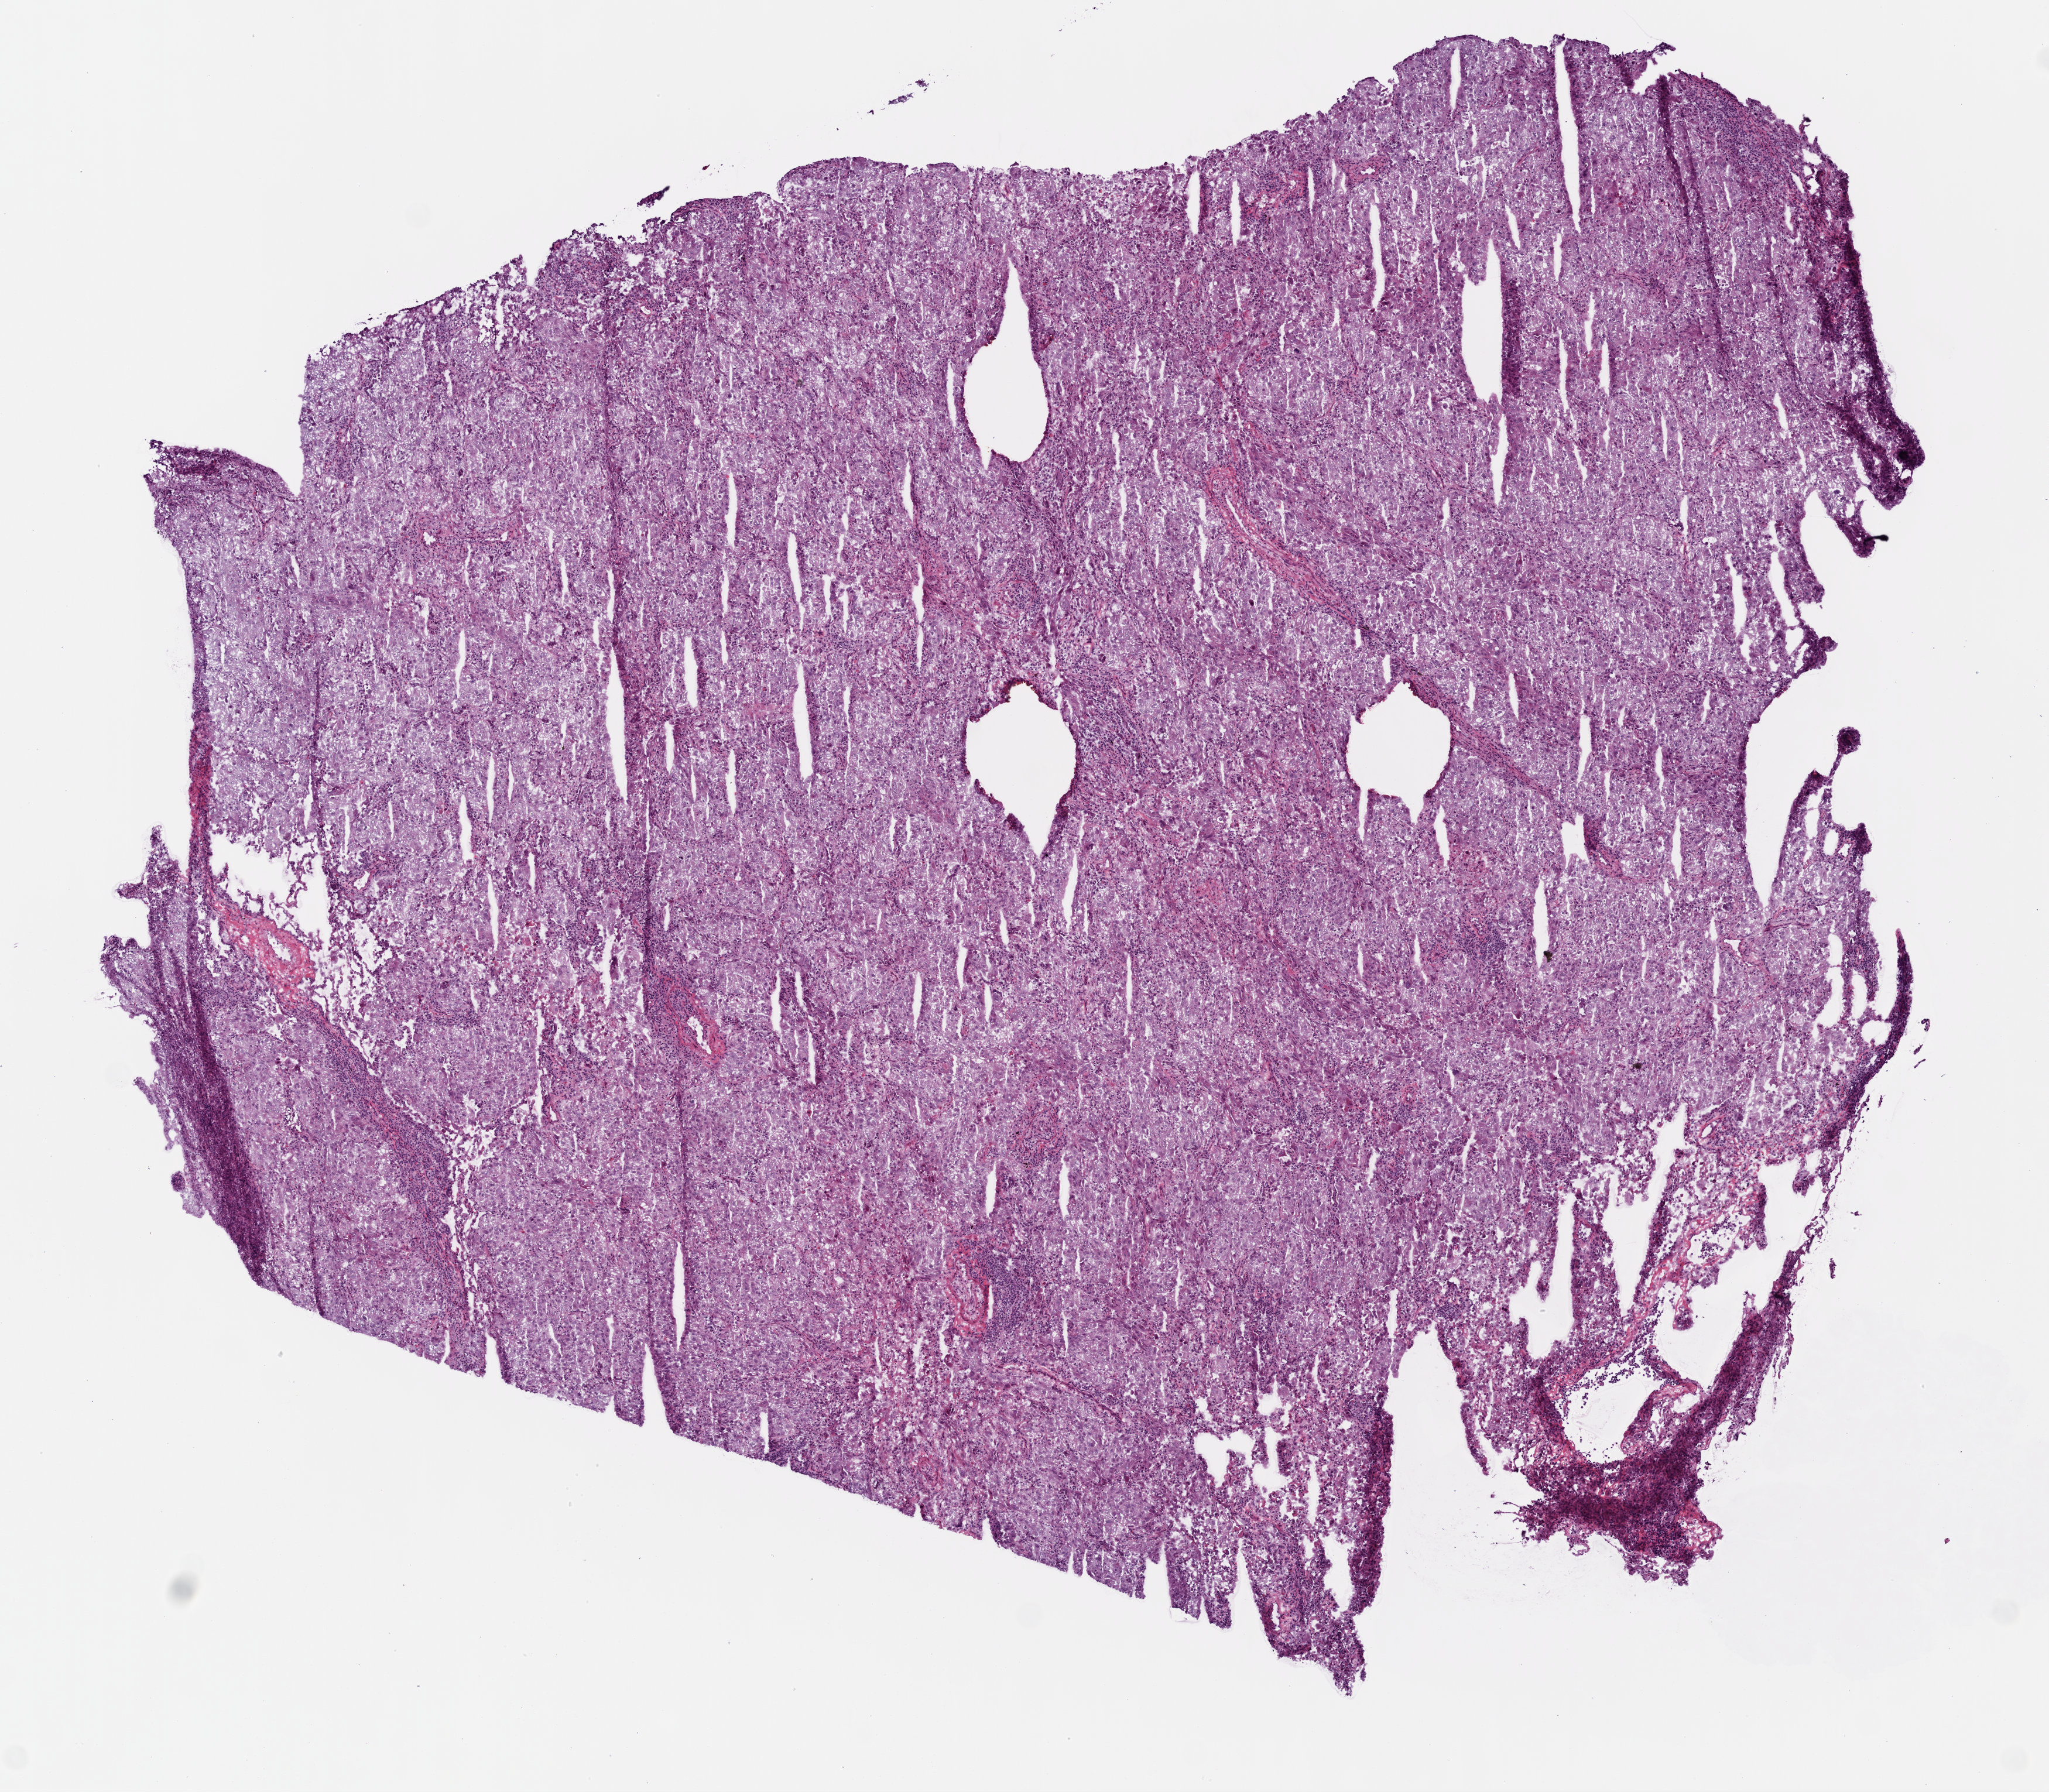
Whole-slide histology image, H&E-stained, whole scanned area (about 7.0 x 6.1 mm, slide scanned at 20x) shown as a low-resolution overview; frozen section from the top of the tissue portion; lung, primary tumour sample. Female patient; age at initial diagnosis 55 years.
Pathologic diagnosis: Solid carcinoma, NOS (upper lobe, lung).